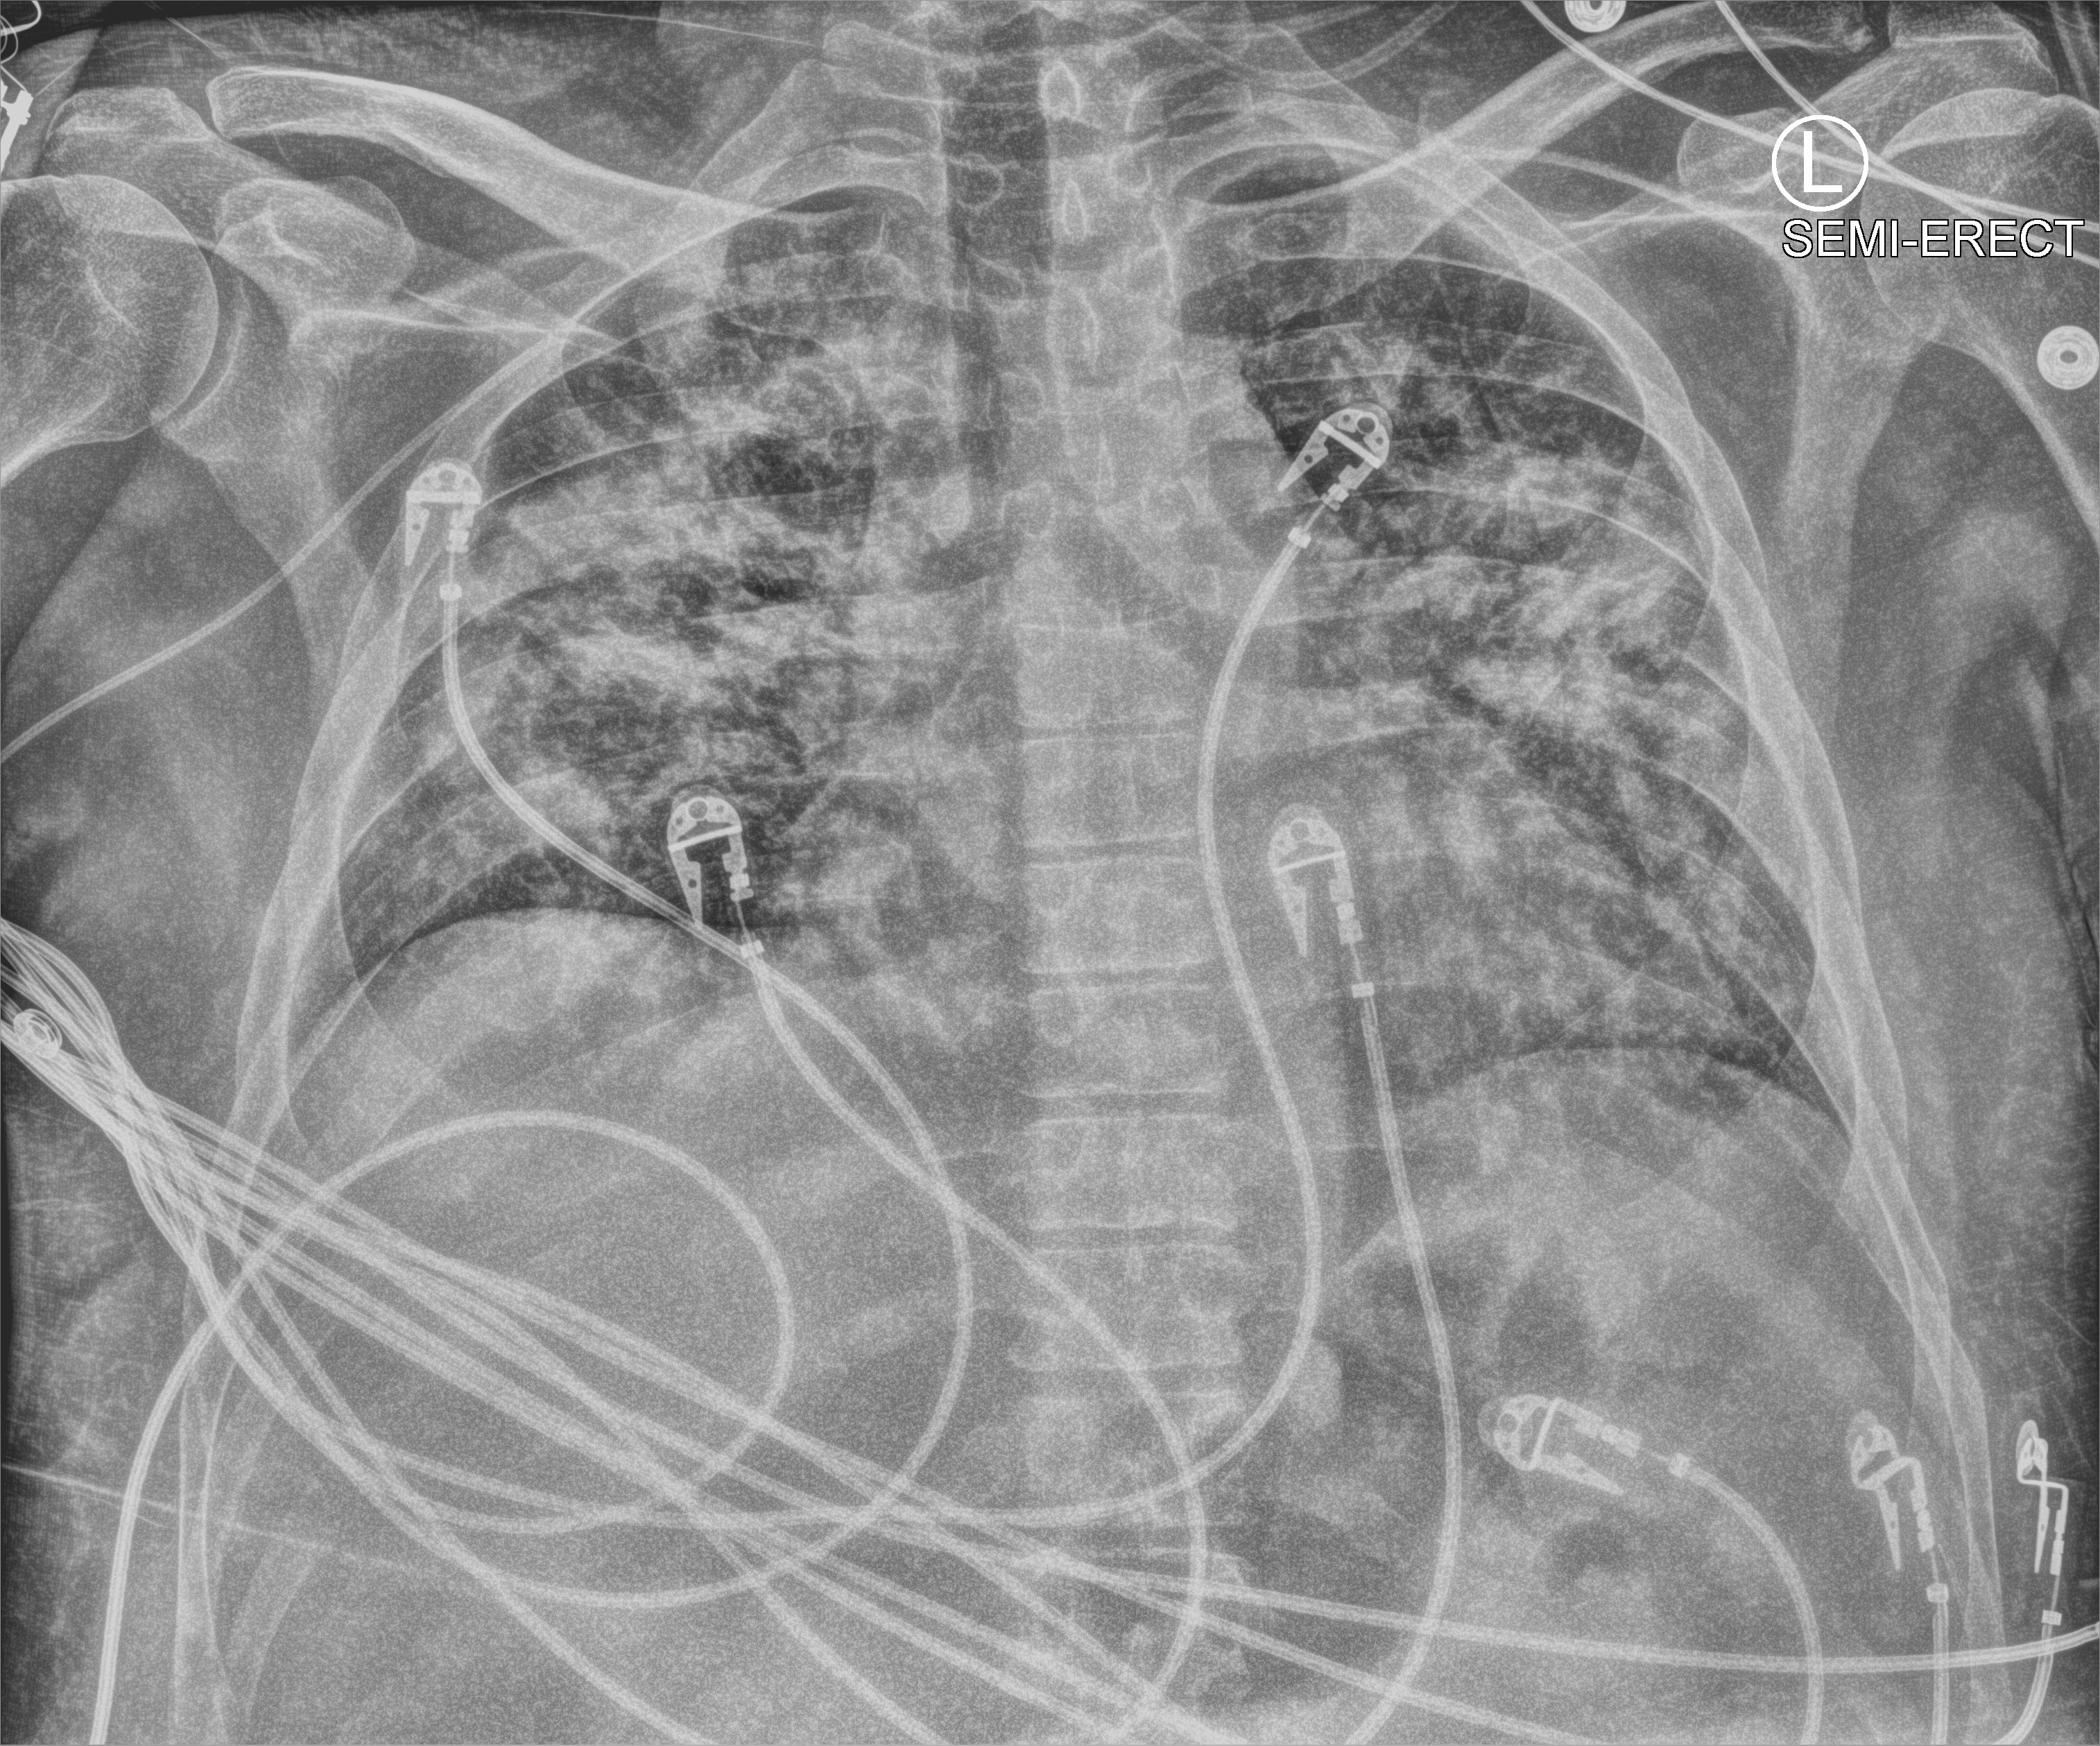
Bedside chest radiograph (computed radiography), anteroposterior (AP) projection. Patient hospitalised with COVID-19; male, aged 18–59 years.
Hospital-stay facts (about this admission, not read from this image; timing relative to this image not recorded):
- length of hospital stay: 20 days
- admitted to intensive care during this hospital stay: yes